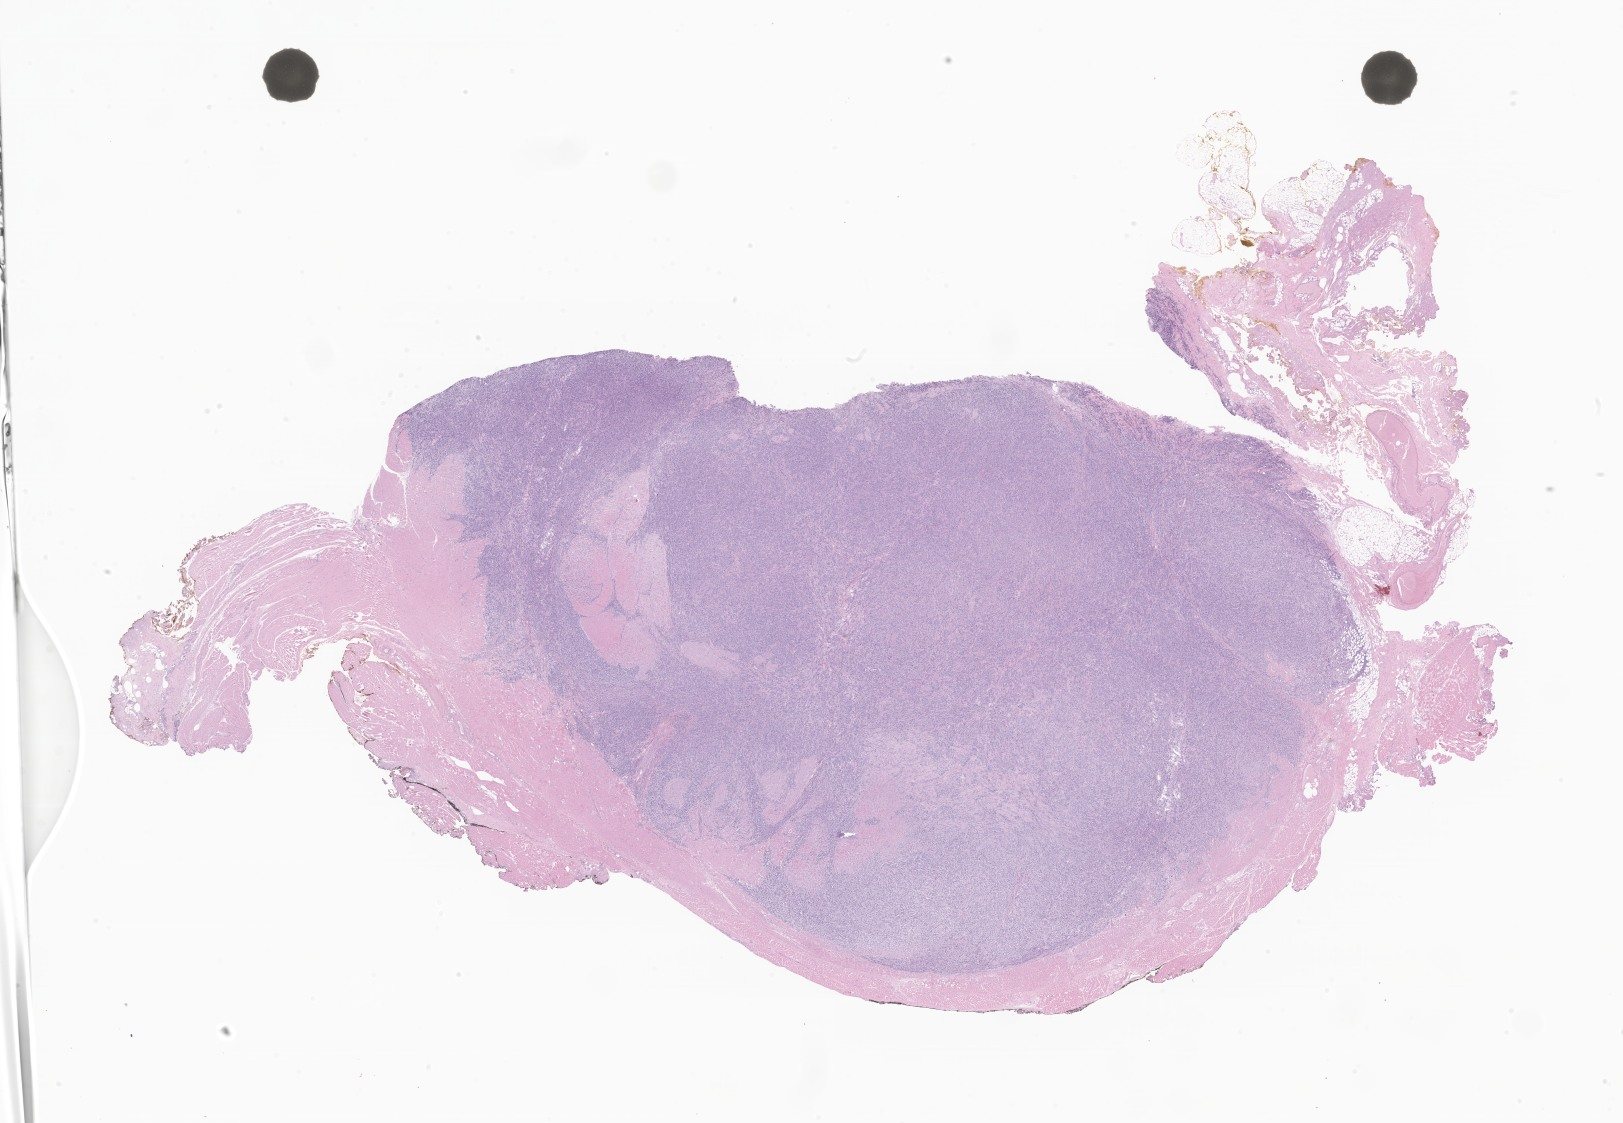
H&E whole-slide image of tumor tissue from the soft tissue, whole scanned area (about 27.4 x 18.9 mm) shown as a low-resolution overview; formalin-fixed, paraffin-embedded (FFPE) tissue. Patient male; age 661 days (about 1.8 years).
* diagnosis: Embryonal rhabdomyosarcoma, NOS